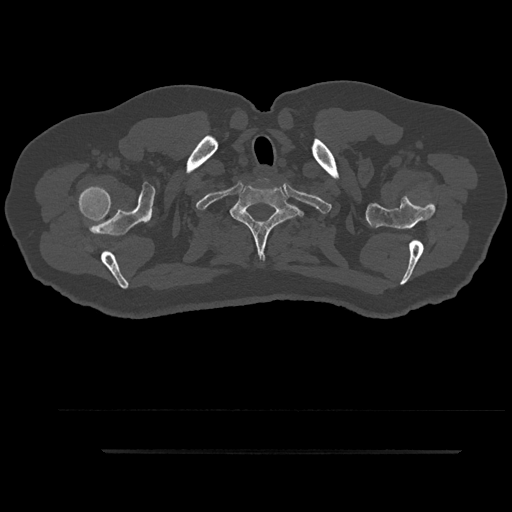
CT including the spine, one axial slice. Slice 796 of 797 in the series (ordered by position). Reconstruction kernel Br40s/3. 120 kVp. Bone window (W 1800 / L 400 HU). 0.5 mm slice thickness. 512 × 512 image matrix, field of view 432 × 432 mm. Patient: male, 63 years. Case-level facts recorded for this patient, not image findings: primary cancer: renal.
Annotated regions visible in this slice (semi-automatic segmentation, software-assisted and operator-edited):
- T1 vertebra: box from (x=231, y=185) to (x=302, y=257) px
- T2 vertebra: (x=215, y=224)–(x=302, y=233)